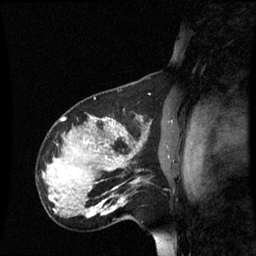
Breast MRI (dynamic contrast-enhanced), one sagittal slice. Position 45 of 60 along the scan axis. Dynamic contrast-enhanced series, image 2 of 3 at this slice position (ordered by acquisition). 1.5 T. TE 4.2 ms, TR 8.9 ms. 256 × 256 image matrix, field of view 220 × 220 mm. Patient: female, 31 years. From the clinical record (not read from this slice): setting: breast cancer imaged before/during neoadjuvant chemotherapy; receptor status: HR-positive, HER2-negative.
Outlined on this slice (semi-automatically segmented with operator editing):
- analysis volume of interest (the breast-tissue region the enhancement analysis was run in; not a lesion): box from (x=90, y=180) to (x=134, y=223) px
- tumour enhancement mask (voxels above the 70 % enhancement threshold inside the analysis volume of interest): (x=90, y=198)–(x=126, y=217)